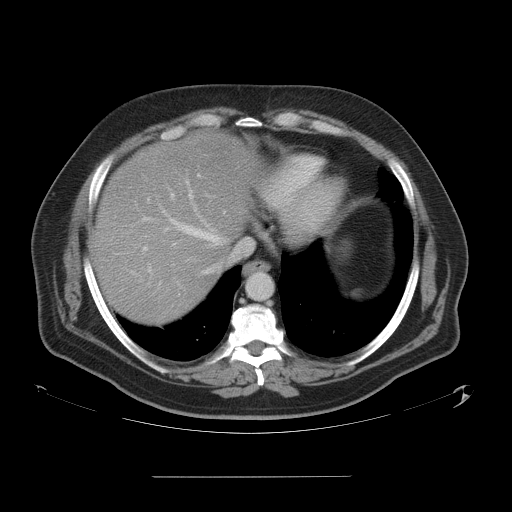
Contrast-enhanced abdominal CT, one axial slice. Position 48 of 58 along the scan axis. 120 kVp. Intravenous contrast given. Soft-tissue window (W 400 / L 40 HU). 5 mm slice thickness. 512 × 512 image matrix, field of view 480 × 480 mm. Male patient, age 63 years. Case-level facts recorded for this patient, not image findings: diagnosis: colorectal cancer liver metastases, imaged before liver resection; multiple liver metastases: no; largest metastasis: 4.2 cm; chemotherapy before resection: yes.
Outlined on this slice (expert manual segmentation):
- hepatic veins: bounding box (x1, y1, x2, y2) in pixels: (132, 181, 246, 286)
- liver: (94, 132, 257, 324)
- planned liver remnant (the part of the liver to remain after resection): (94, 206, 223, 324)
- portal vein (with intrahepatic branches): (143, 174, 200, 251)